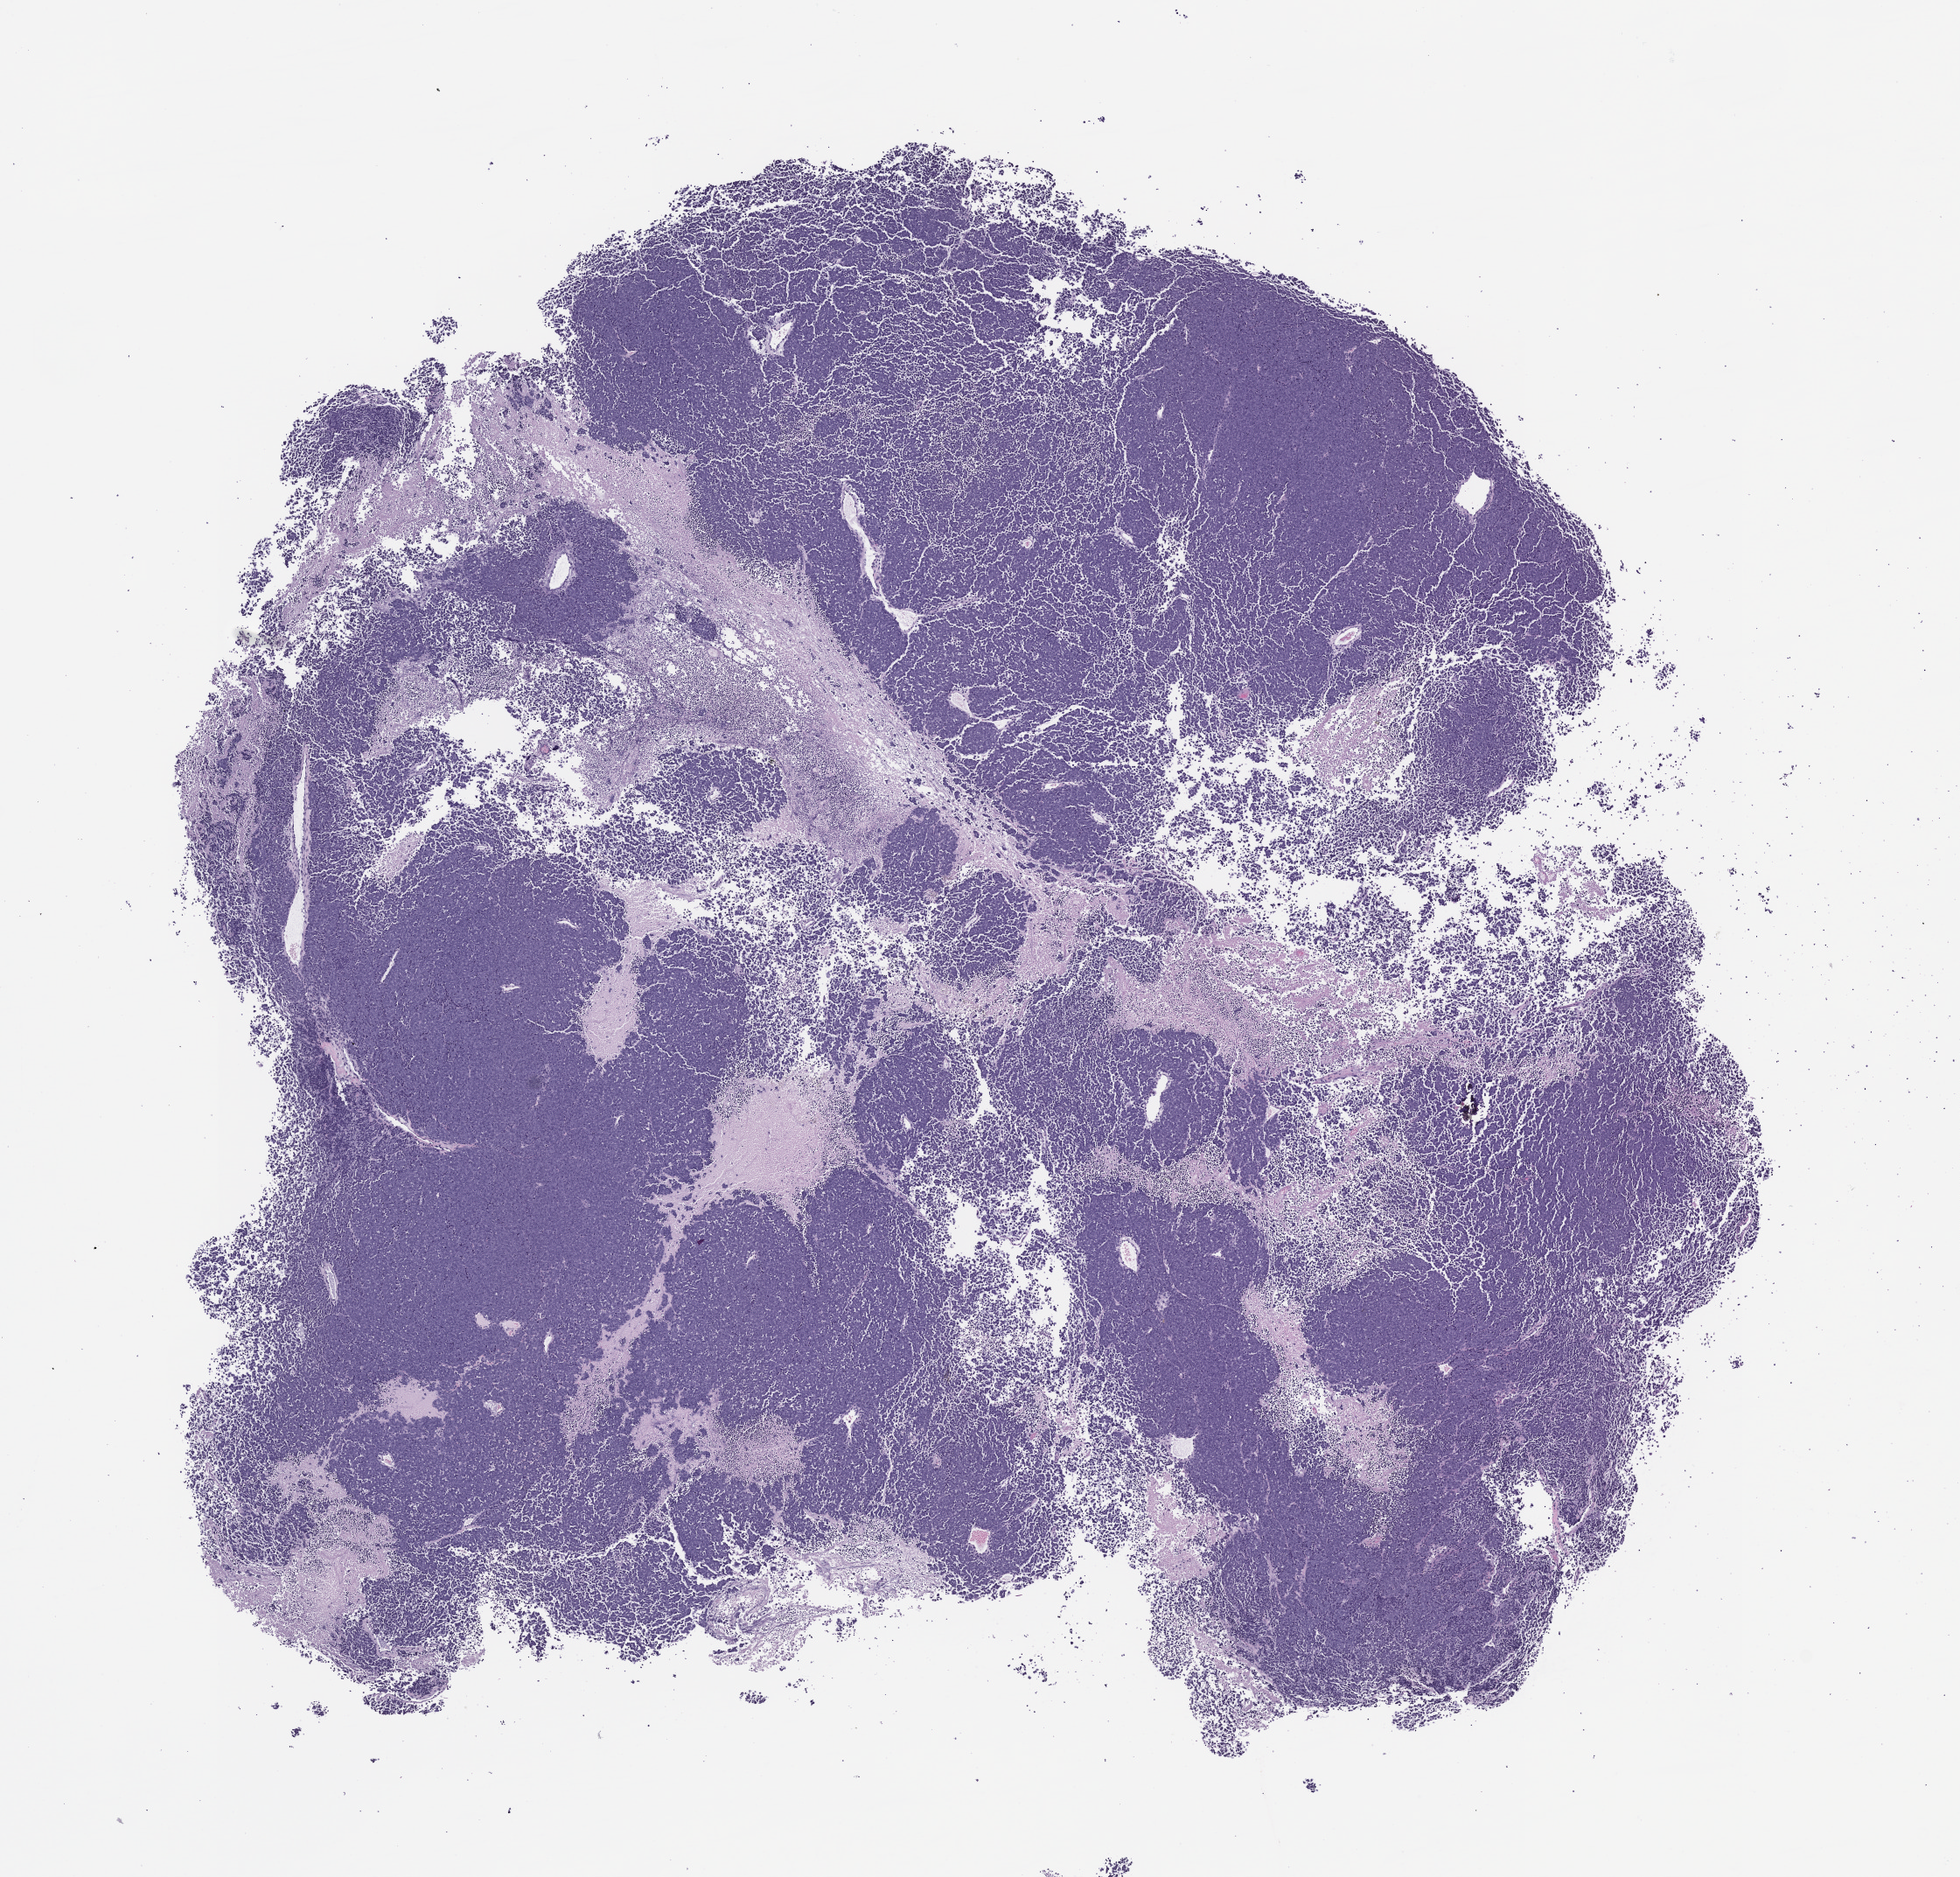
Whole-slide image, haematoxylin and eosin: patient-derived xenograft (human tumor grown in a mouse), passage 1, low-resolution overview of the scanned area, about 9.0 x 8.6 mm, formalin-fixed, paraffin-embedded (FFPE) tissue, tumor site category: endocrine.
Originating patient diagnosis: Merkel Cell Carcinoma.